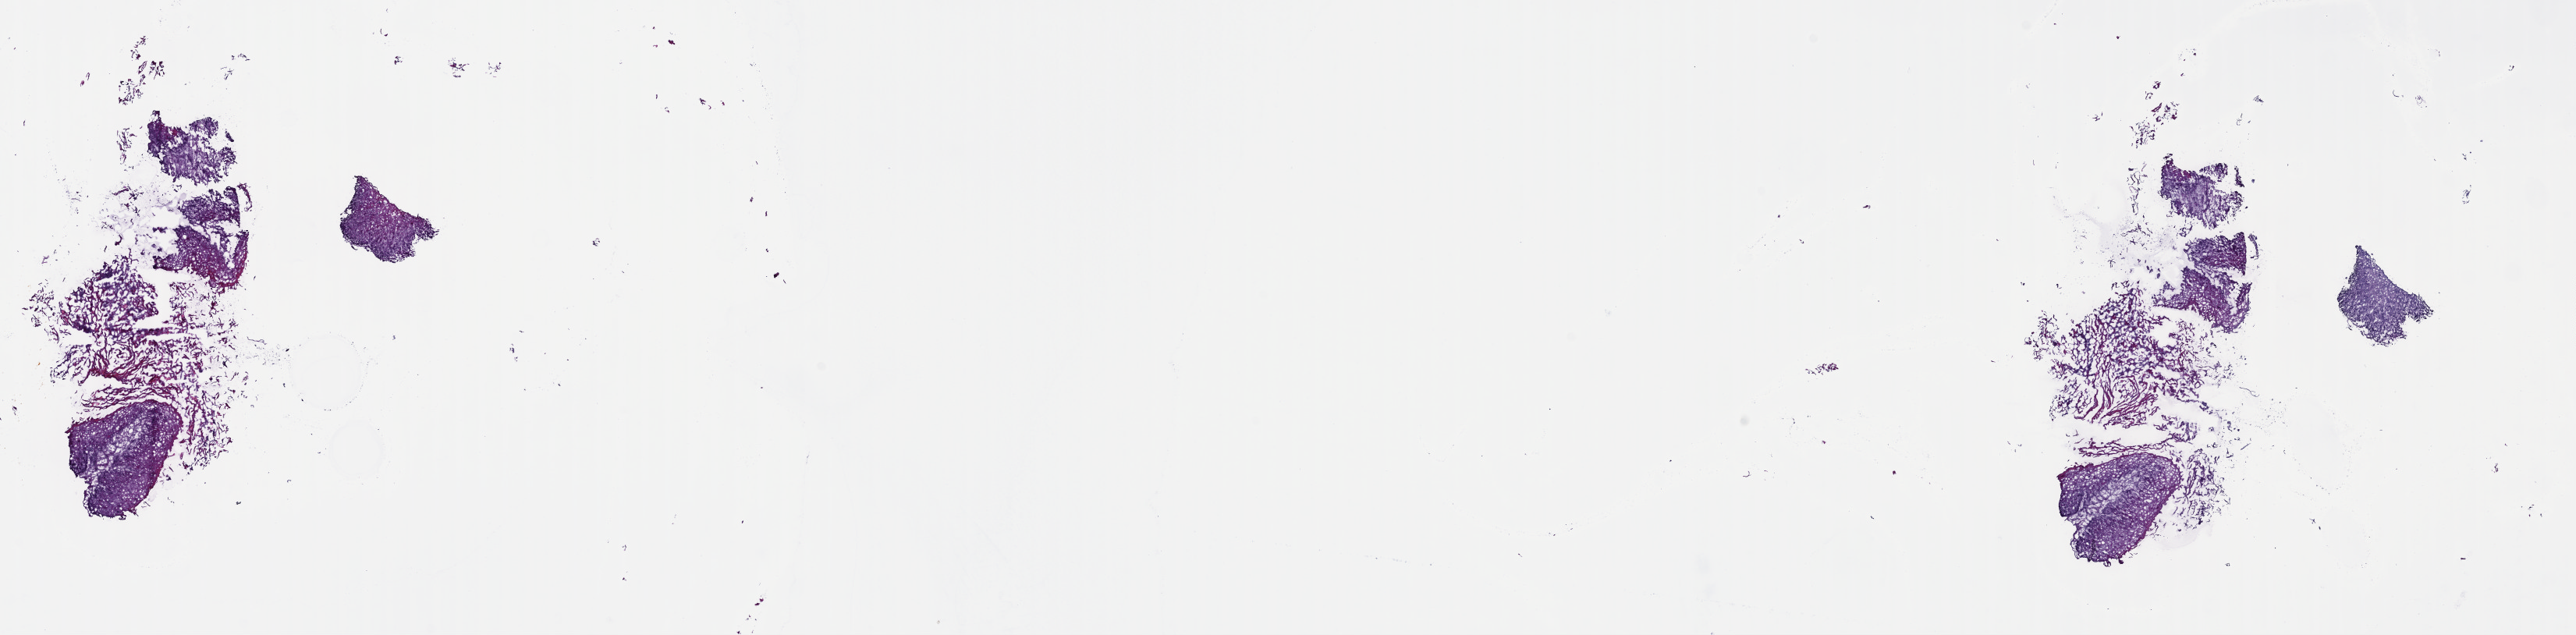
Whole-slide histology image, H&E, low-resolution overview of the scanned area, about 26.0 x 6.4 mm (slide scanned at 40x); frozen section from the top of the tissue portion; head and neck, primary tumour sample. Patient: male, age at initial diagnosis 69 years. Histologic grade: G1 (well differentiated). Pathologist review of this section (percent, as recorded): tumour cells 80%, tumour nuclei 92%, normal cells 0%, stromal cells 10%, necrosis 10%. Infiltration values recorded for this section: lymphocyte infiltration 4%, monocyte infiltration 0%, neutrophil infiltration 1%.
• AJCC pathologic stage: IVA (7th edition)
• pathologic diagnosis: Squamous cell carcinoma, NOS